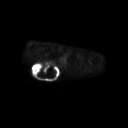
FDG PET of an extremity soft-tissue mass (from a PET/CT study), one axial slice. 3.27 mm slice thickness. 128 × 128 image matrix, field of view 700 × 700 mm. Patient: male, 61 years. From the clinical record (not read from this slice): histological type: pleiomorphic spindle cell undifferentiated; grade: high; site of the primary tumour: right parascapusular.
Structures marked on this image (expert contour drawn on MRI and transferred to this co-registered scan by the dataset authors):
- gross tumour volume including surrounding oedema: bounding box [x1, y1, x2, y2] px = [32, 62, 60, 78]
- gross tumour volume (mass): [32, 63, 58, 78]